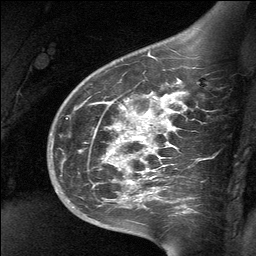
Breast MRI (dynamic contrast-enhanced), one sagittal slice; dynamic contrast-enhanced study with each time point stored as its own series, time point 2 of 3 at this slice position (early post-contrast, ordered by acquisition time); 1.5 T; TE 4.8 ms, TR 27 ms; 2 mm slice thickness; 256 × 256 image matrix, field of view 200 × 200 mm. Patient: female, 39 years. From the clinical record (not read from this slice): setting: breast cancer imaged before/during neoadjuvant chemotherapy; receptor status: HER2-positive.
Structures marked on this image (semi-automatic segmentation, software-assisted and operator-edited):
- analysis volume of interest (the breast-tissue region the enhancement analysis was run in; not a lesion): bounding box <70,69,202,224> (left, top, right, bottom; pixels)
- tumour enhancement mask (voxels above the 90 % enhancement threshold inside the analysis volume of interest): <111,97,175,178>